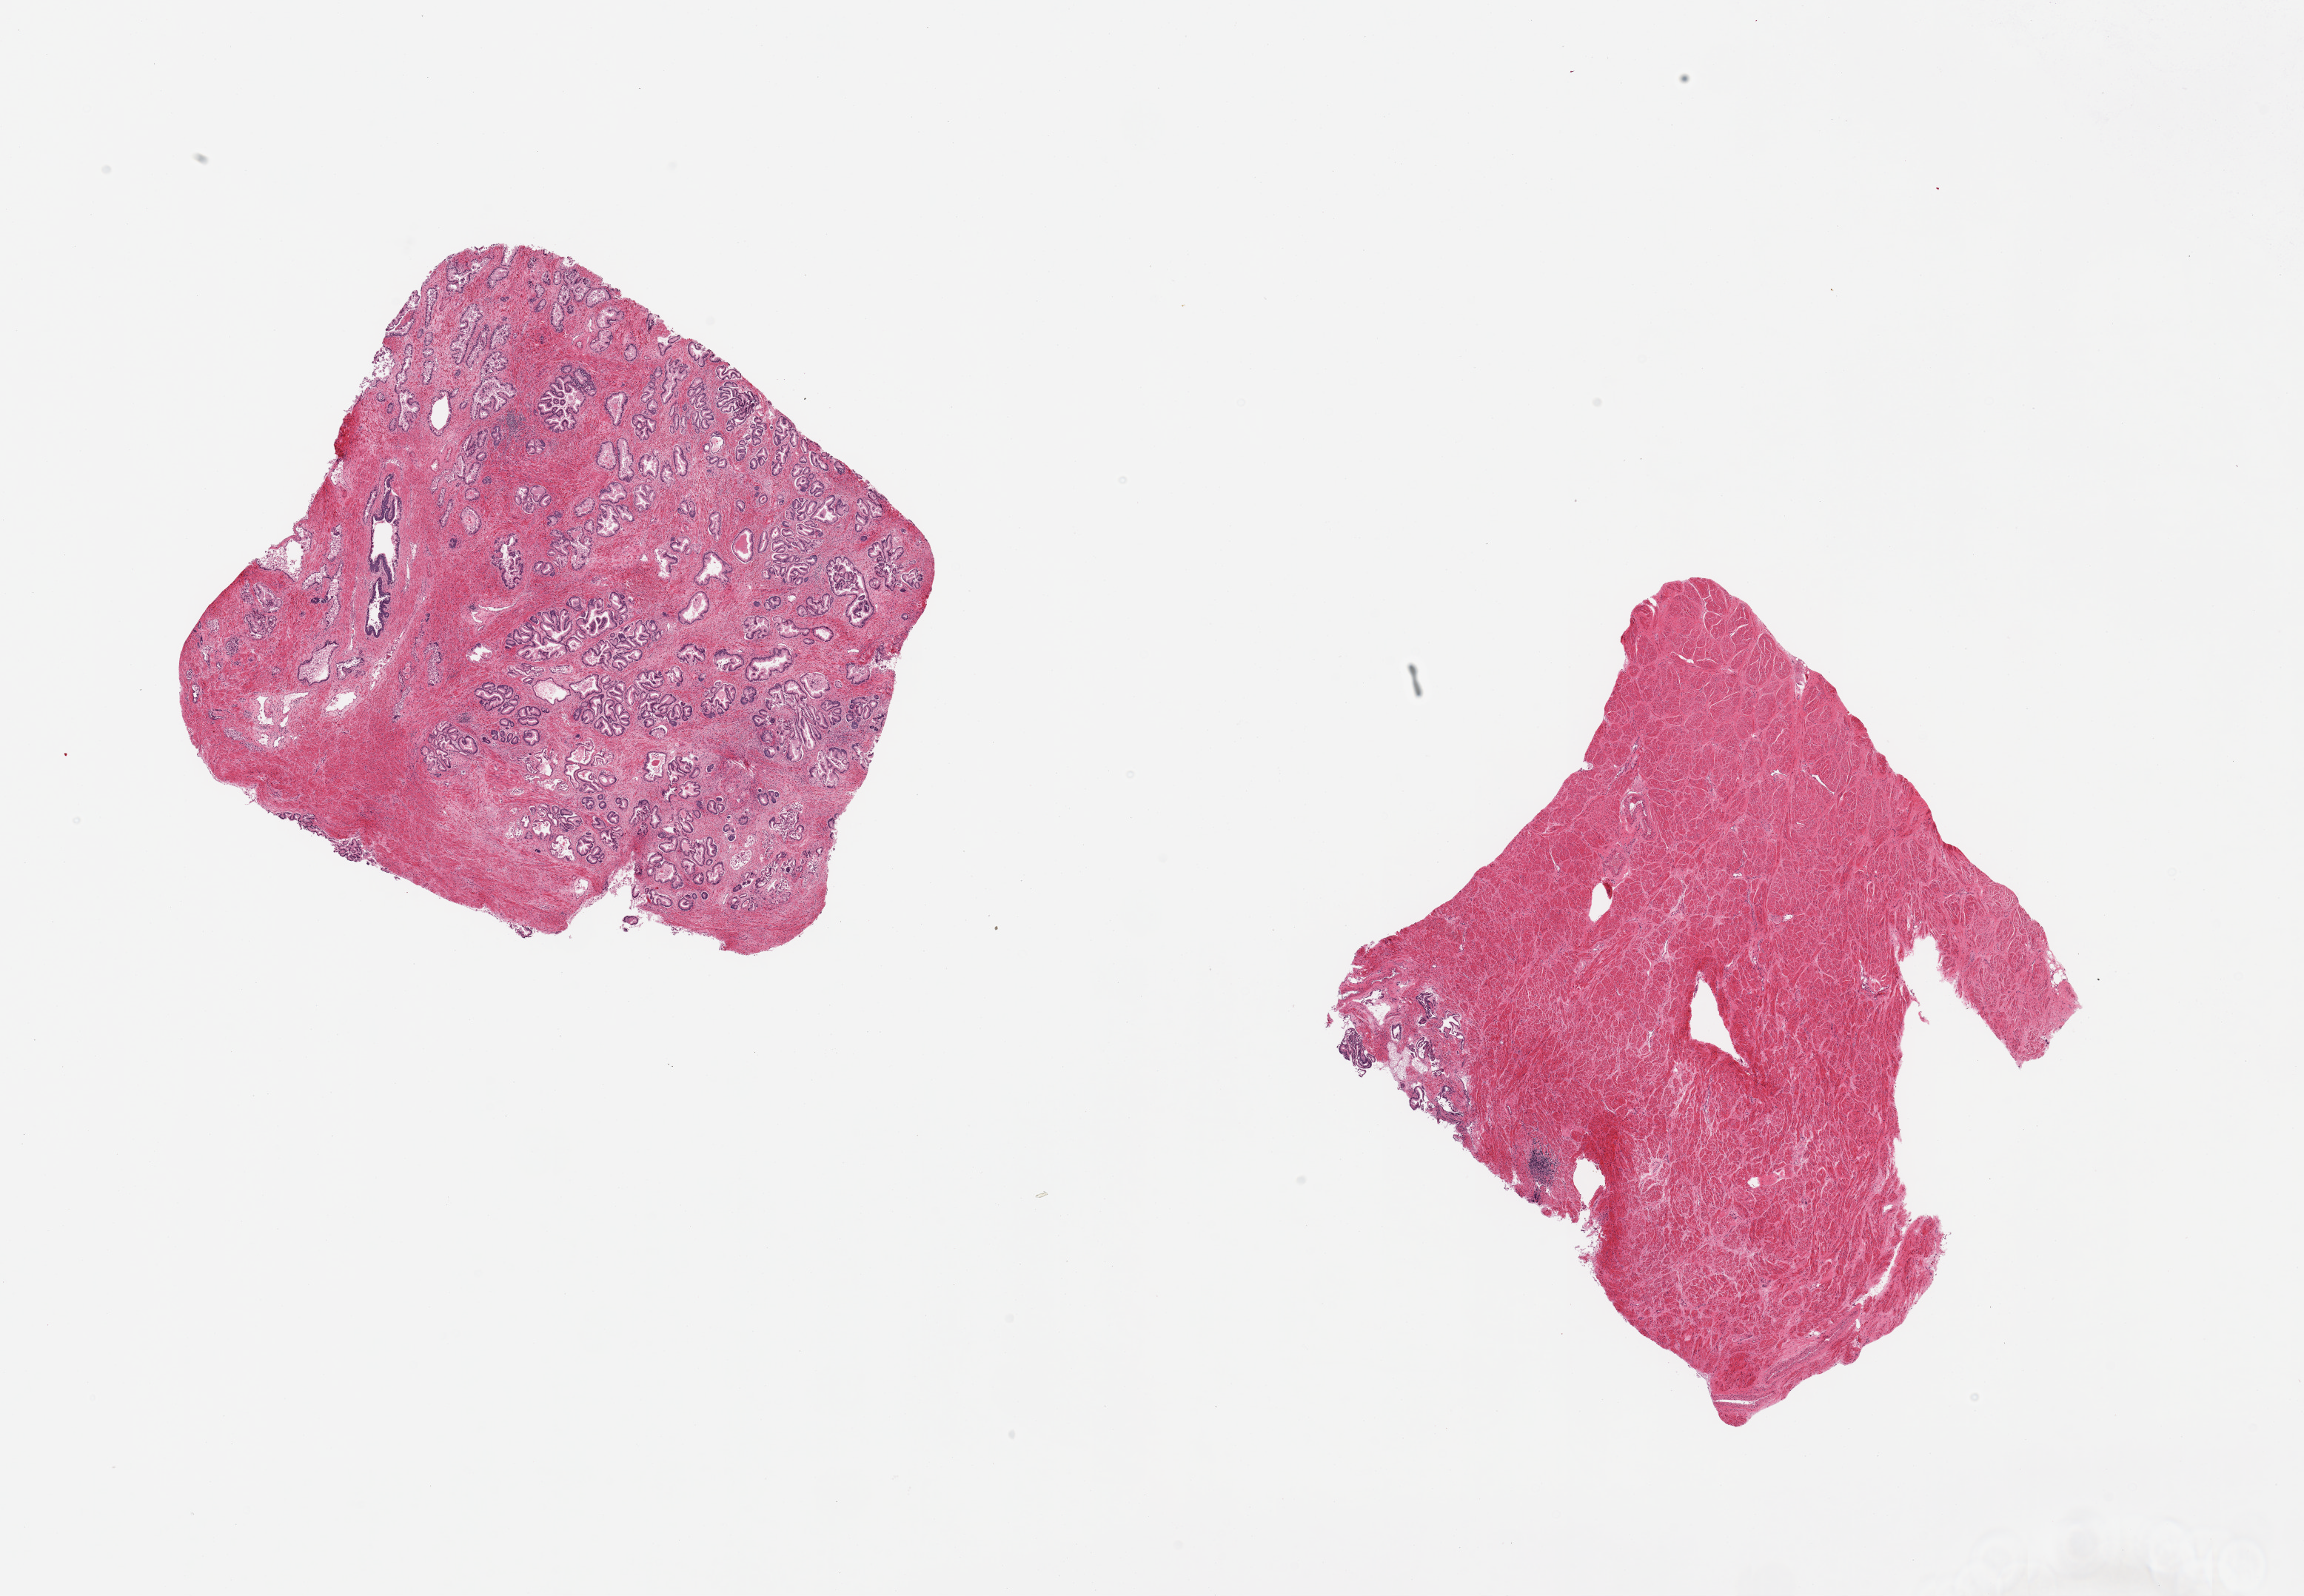
Haematoxylin and eosin whole-slide image, low-resolution overview of the scanned area, about 24.6 x 17.1 mm. PAXgene-fixed, paraffin-embedded tissue. Sampled site (target tissue): prostate. Donor tissue sample. Donor sex: male.
Reviewer comment on this tissue sample: 2 pieces: 1 glandular, the other 90% stromal.